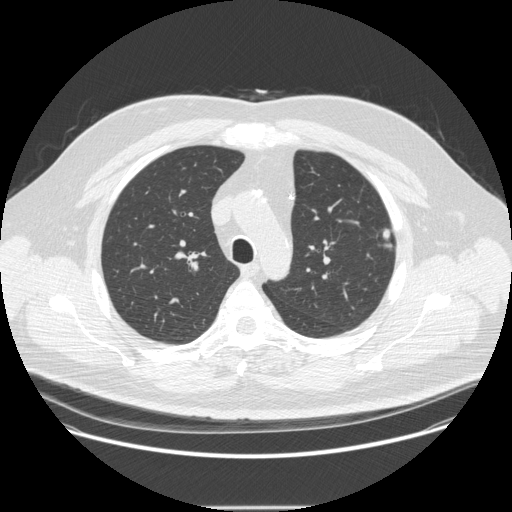
Low-dose screening chest CT, axial slice. Second screening round (one year after baseline). Lung window (W 1500 / L -600 HU). Standard (soft-tissue) reconstruction kernel (STANDARD). Slice 75 of 251 in the series. 512 × 512 image matrix. Male, age 55 years at enrolment. Former smoker at enrolment.
• Expert-annotated lung lesion, bounding box [x1, y1, x2, y2] px = [373, 227, 405, 250].
• The screening reader recorded 2 non-calcified nodules or masses ≥4 mm on this exam (left upper lobe, left upper lobe); which of them this box marks is not recorded.
• Official screen result: positive, other.
• Participant outcome: lung cancer diagnosed 60 days after this screen — adenocarcinoma, NOS, left upper lobe, moderately differentiated (G2), stage IA (AJCC 6th edition), 9 mm at pathology.